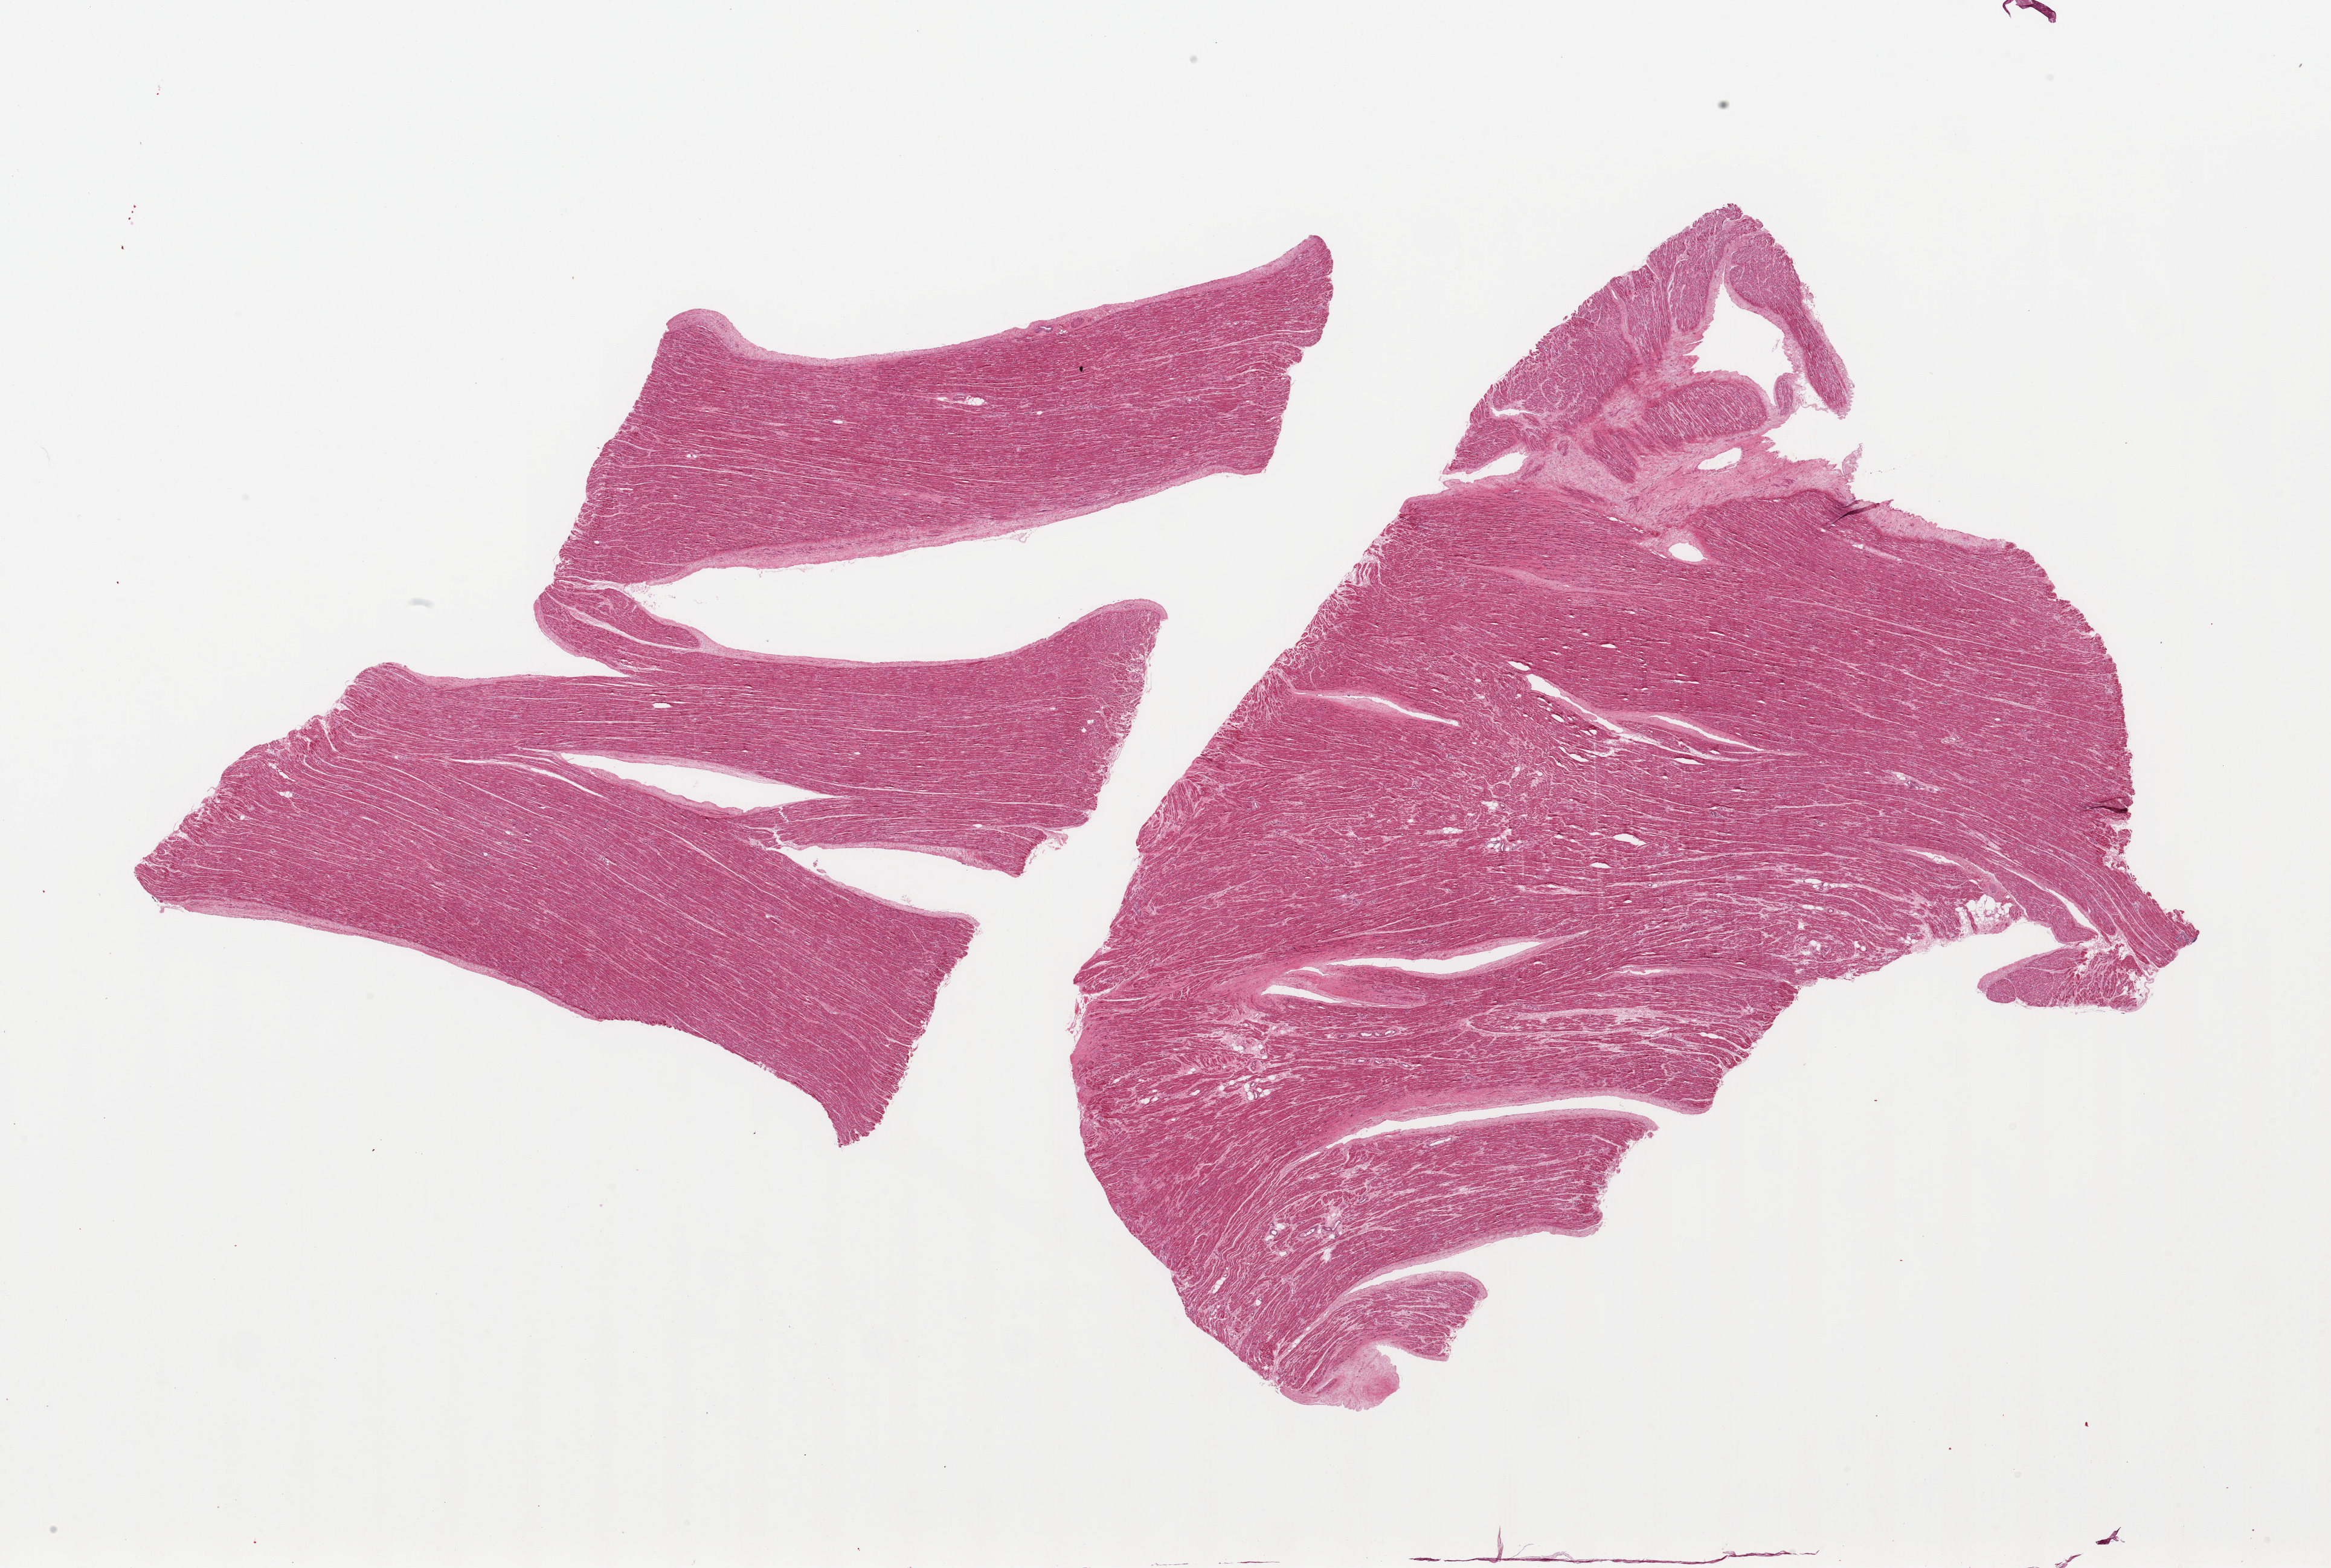
Whole-slide image, haematoxylin and eosin stain — whole scanned area (about 30.5 x 20.5 mm, from a 20x scan) shown as a low-resolution overview, PAXgene-fixed, paraffin-embedded tissue, target tissue: auricular appendage, donor tissue sample. Donor: male.
Pathologist's review note for this sample: 2 pieces; <5% fibrous content.